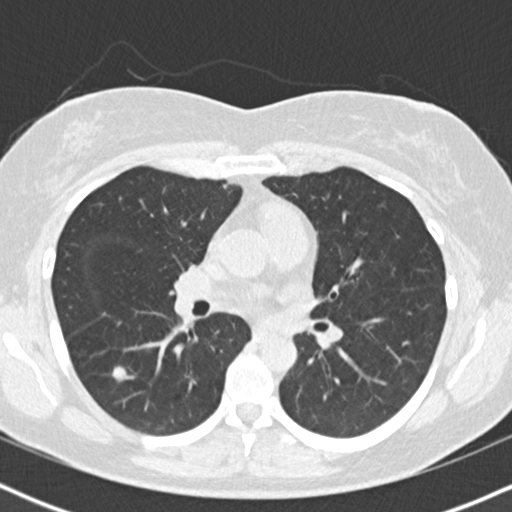
Chest CT (low-dose screening protocol), one axial image. Baseline screening round. Lung window (W 1500 / L -600 HU). Standard (soft-tissue) reconstruction kernel (B30f). 120 kVp. Female, age 55 years at enrolment. Former smoker at enrolment.
- Expert-annotated lung lesion, bounding box <89,347,145,395> (left, top, right, bottom; pixels).
- The exam's reader record, not a measurement of the box and not confirmed to be the same lesion: non-calcified nodule or mass ≥4 mm, right lower lobe, 8 × 8 mm, poorly defined margins, soft tissue attenuation.
- Official screen result: positive, change unspecified: nodule(s) >= 4 mm or enlarging nodule(s), mass(es), or other non-specific abnormalities suspicious for lung cancer.
- Participant outcome: lung cancer diagnosed 14 days after this screen — bronchiolo-alveolar adenocarcinoma, NOS, right lower lobe, well differentiated (G1), stage IA (AJCC 6th edition), 12 mm at pathology.